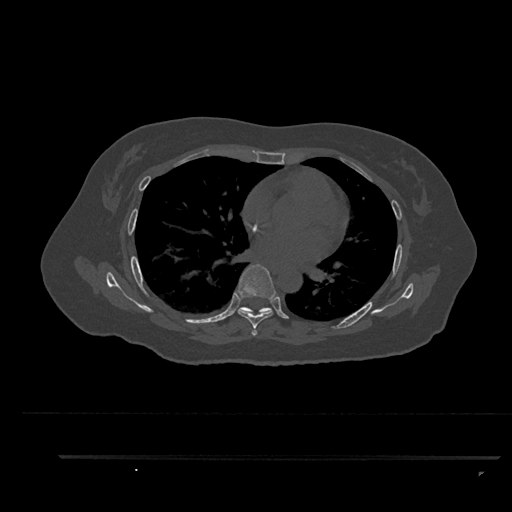
CT including the spine, one axial slice. Slice 542 of 797 in the series (ordered by position). Reconstruction kernel Br40s/3. 120 kVp. Bone window (W 1800 / L 400 HU). 0.5 mm slice thickness. 512 × 512 image matrix, field of view 408 × 408 mm. Female patient, age 44 years. Case-level facts recorded for this patient, not image findings: primary cancer: renal; vertebrae with lytic lesions (as recorded): L1.
Structures marked on this image (semi-automatically segmented with operator editing):
- T6 vertebra: bounding box [x1, y1, x2, y2] px = [235, 264, 276, 336]
- T7 vertebra: [239, 307, 272, 315]